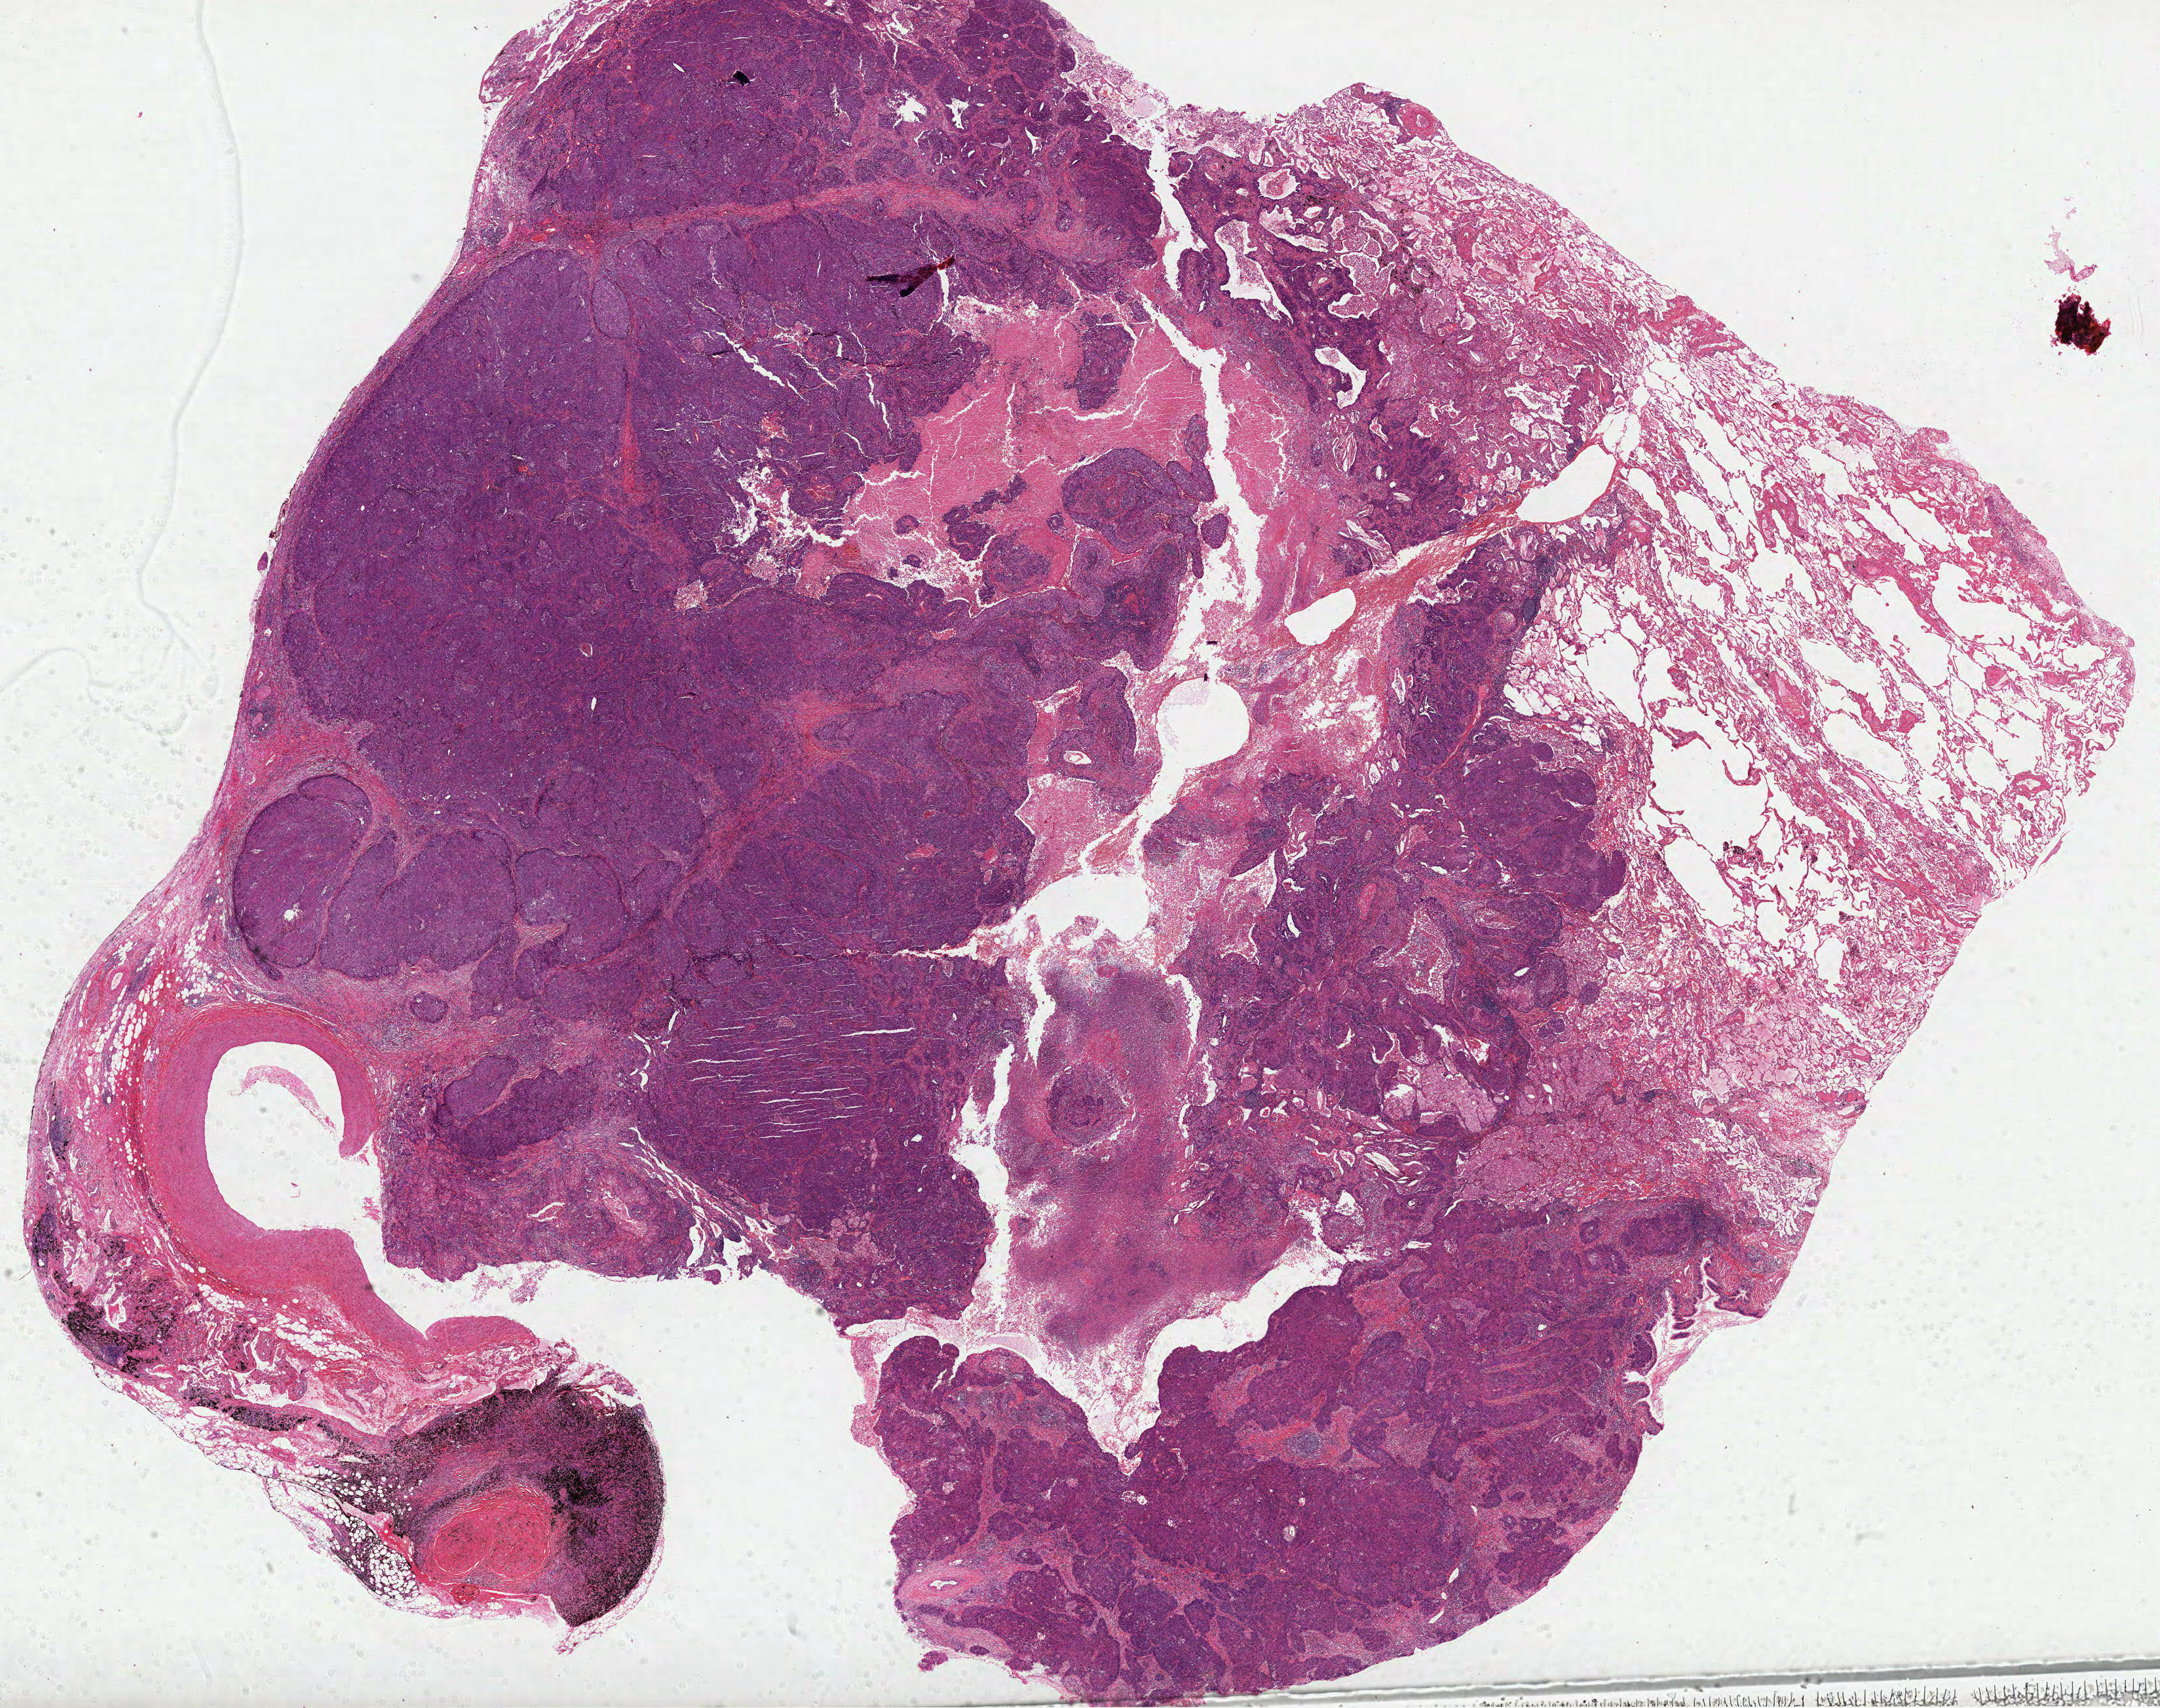
Hematoxylin and eosin (H&E) stained whole-slide image — a low-resolution overview of the entire scanned area, about 26.6 x 21.0 mm, formalin-fixed paraffin-embedded (FFPE) diagnostic section, sample: primary tumour, lung. Male, age 74 years at initial diagnosis.
Laterality: right. TNM: T1 N1 M0. Pathologic diagnosis: Squamous cell carcinoma, NOS. AJCC pathologic stage: IIA.